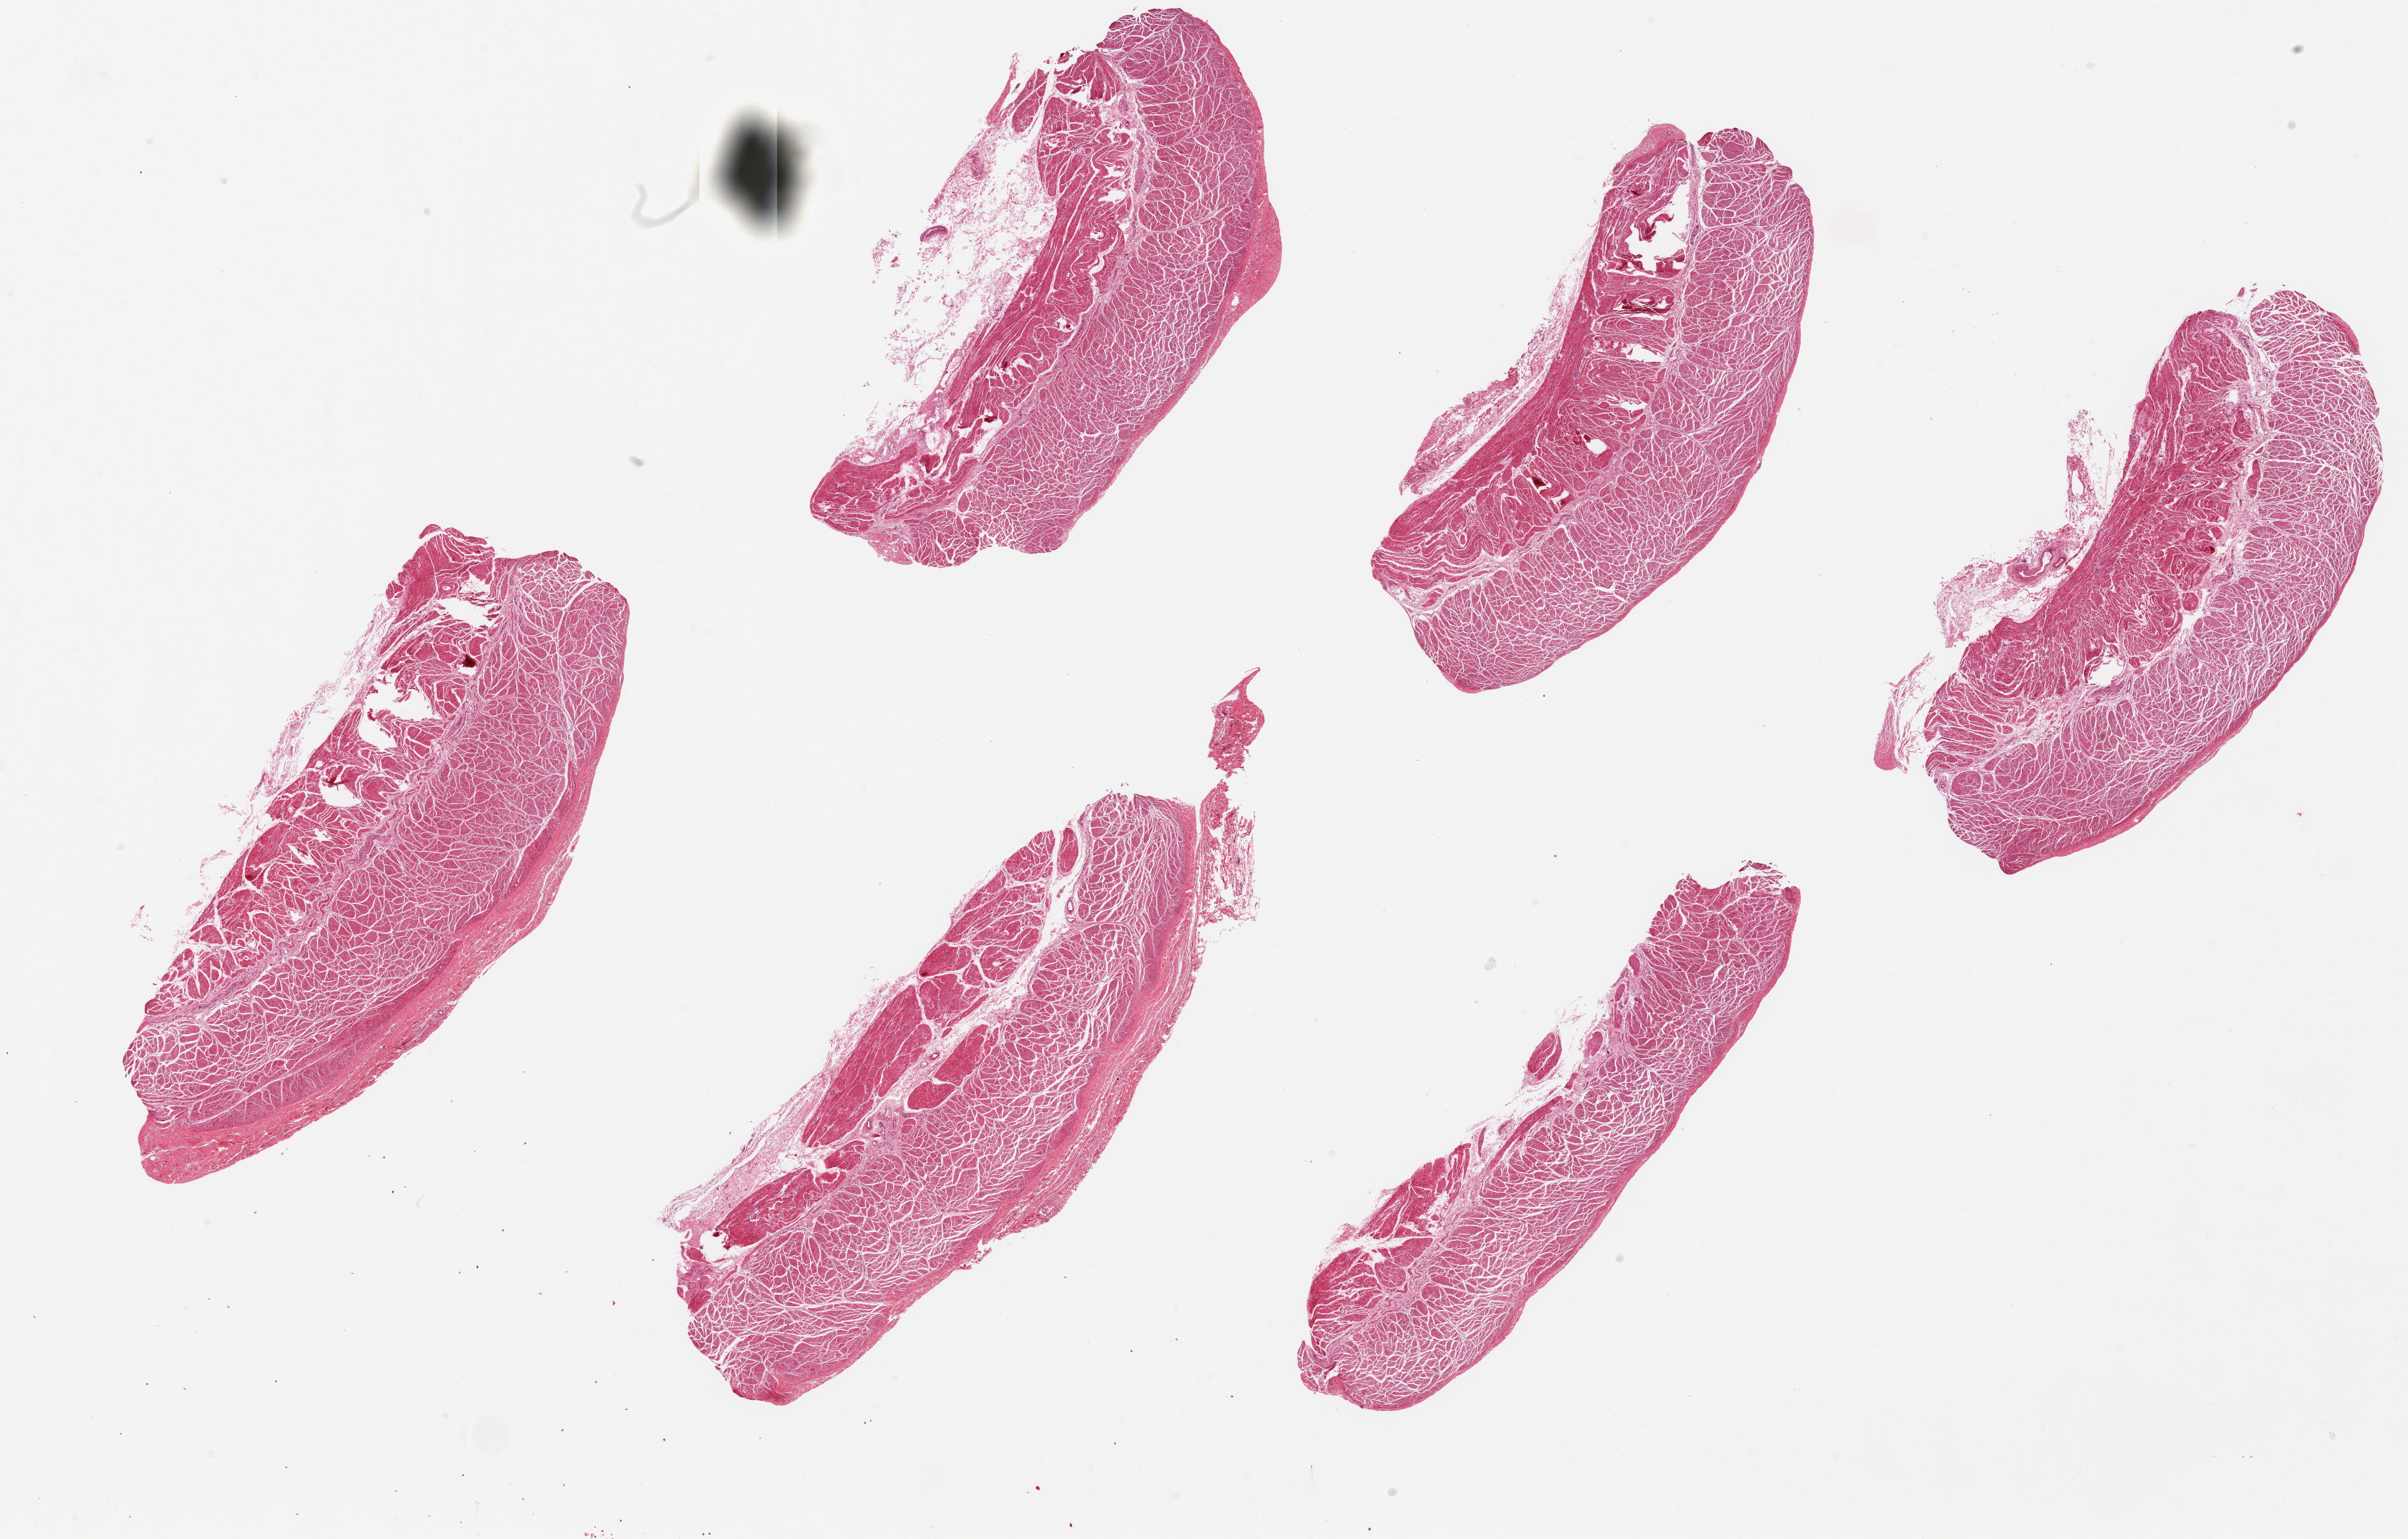
H&E whole-slide image, brightfield — a low-resolution overview of the entire scanned area, about 30.5 x 19.5 mm; PAXgene-fixed, paraffin-embedded tissue; target tissue: esophageal muscle; donor tissue sample. Donor: female.
Reviewer comment on this tissue sample: 6 pieces, ~8.5x3mm.